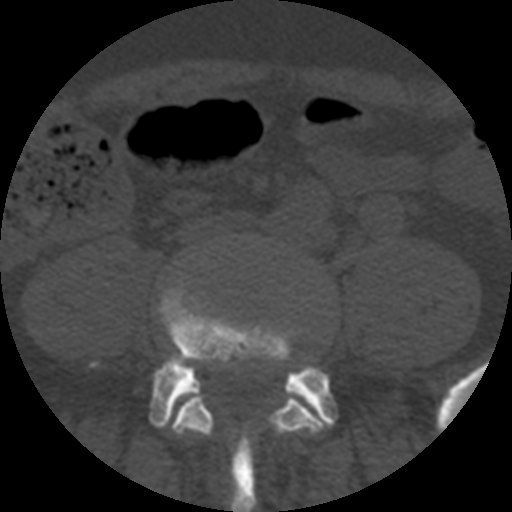
CT including the spine, one axial slice; slice 75 of 508 in the series (ordered by position); reconstruction kernel STANDARD; 120 kVp; bone window (W 1800 / L 400 HU); 1.25 mm slice thickness; 512 × 512 image matrix, field of view 160 × 160 mm. Patient age 57 years. From the clinical record (not read from this slice): primary cancer: prostate.
Annotated regions visible in this slice (semi-automatically segmented with operator editing):
- L4 vertebra: bounding box (x1, y1, x2, y2) in pixels: (172, 389, 325, 436)
- L5 vertebra: (150, 290, 336, 512)